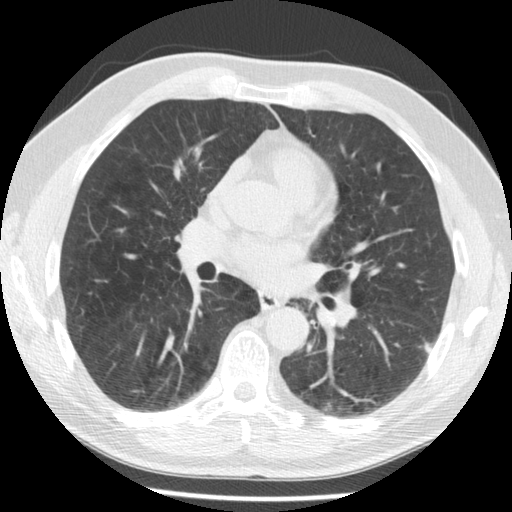
Axial slice from a low-dose chest CT screening exam, second screening round (one year after baseline), lung window (W 1500 / L -600 HU), 2.5 mm slice thickness, standard (soft-tissue) reconstruction kernel (STANDARD), slice 64 of 115 in the series. Male, age 57 years at enrolment. Former smoker at enrolment.
Expert reader's lesion annotation, bounding box [x1, y1, x2, y2] px = [405, 325, 447, 365]. Reader record for this screening exam (exam-level; its link to the box is not recorded): non-calcified nodule or mass ≥4 mm, left lower lobe, 6 × 5 mm, poorly defined margins, soft tissue attenuation, pre-existing on the prior screen: yes; interval growth: no. Participant outcome: lung cancer diagnosed 427 days after this screen (after the third annual screen) — non-small cell carcinoma, left lower lobe, stage IV (AJCC 6th edition), 13 mm at pathology.